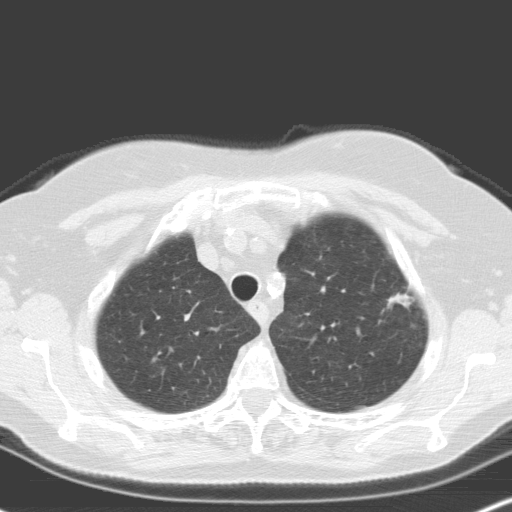
Low-dose screening chest CT, one axial slice; slice 137 of 160 in the series (ordered by position); 120 kVp; lung window (W 1500 / L -600 HU); 3.2 mm slice thickness; 512 × 512 image matrix, field of view 316 × 316 mm.
Annotated regions visible in this slice (outlined manually by an expert reader):
- lesion 2 (nodule): bounding box [x1, y1, x2, y2] px = [387, 292, 412, 307]